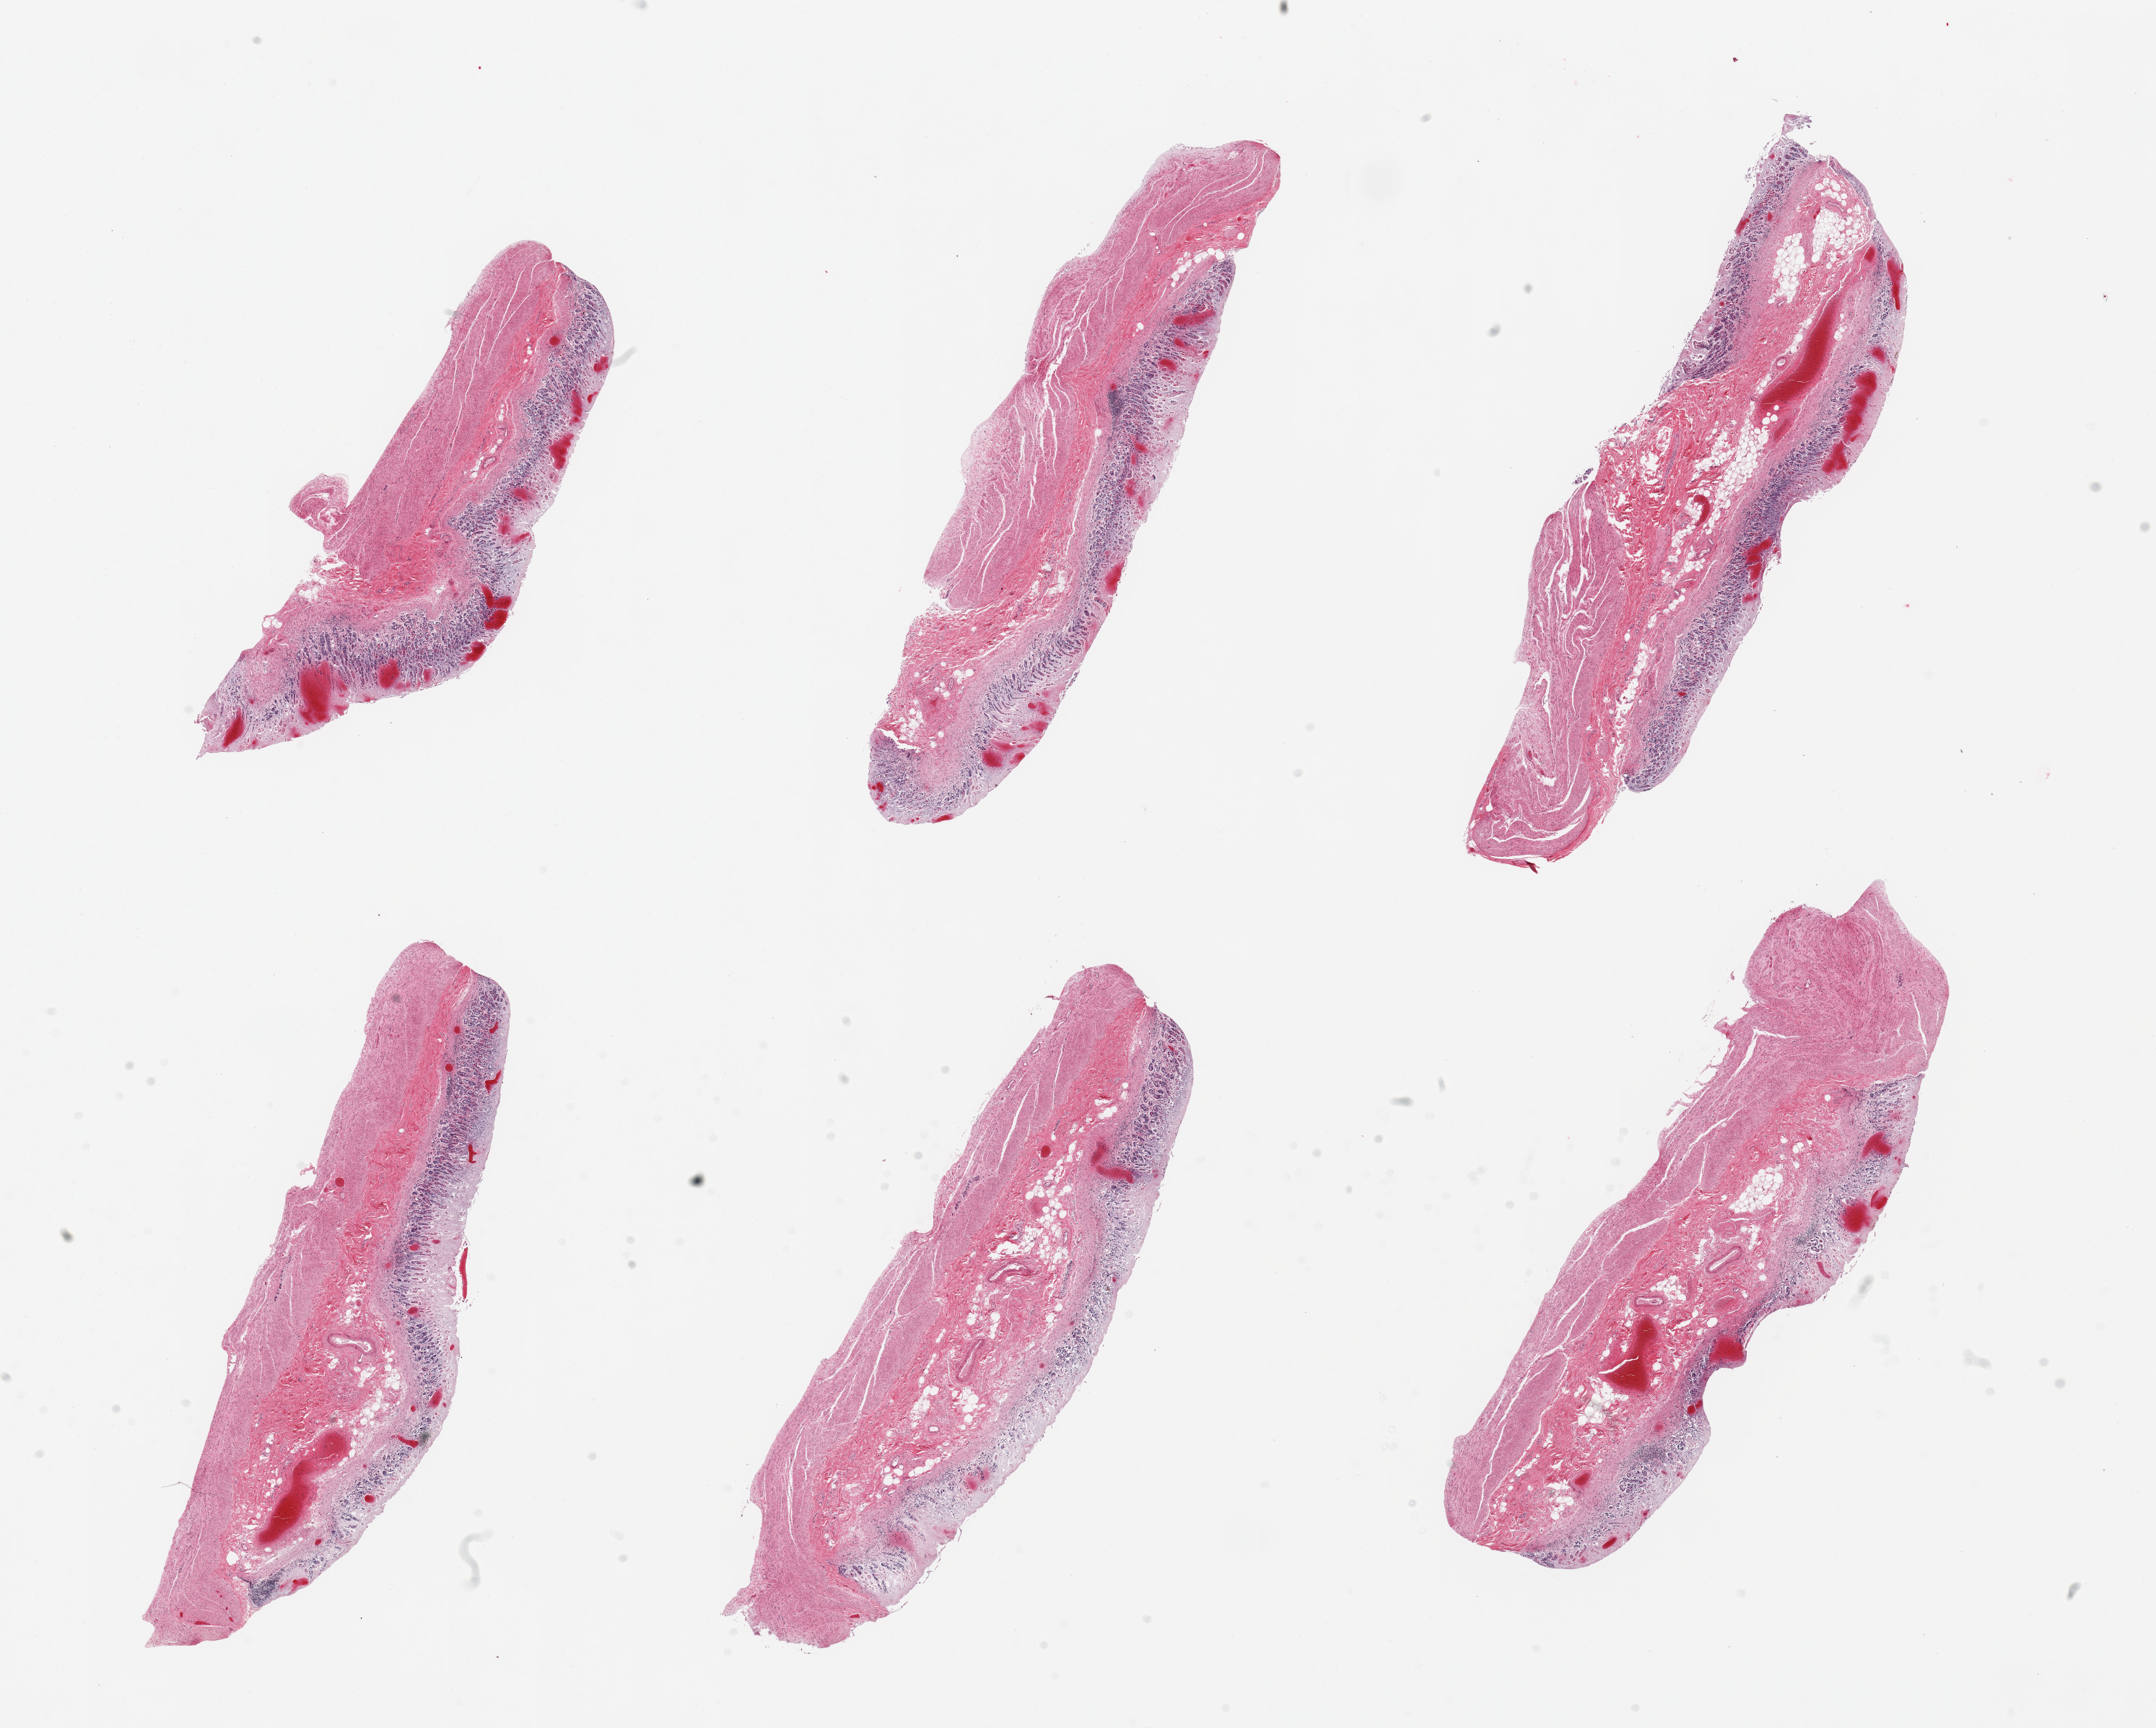
Hematoxylin and eosin (H&E) whole-slide image — low-resolution overview of the scanned area, about 23.6 x 18.9 mm; PAXgene-fixed, paraffin-embedded tissue; target tissue: stomach; donor tissue sample. Female donor.
Reviewer comment on this tissue sample: 6 pieces; full thickness sections with moderate to severe mucosal autolysis, congestion, muscularis is moderatley autolyzed.